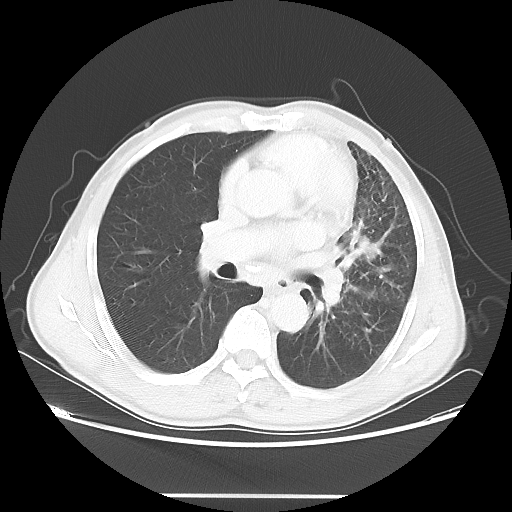
Chest CT, one axial slice. Slice 28 of 55 in the series (ordered by position). Reconstruction kernel LUNG. Lung window (W 1500 / L -600 HU). 5 mm slice thickness. 512 × 512 image matrix, field of view 398 × 398 mm. Patient: male, 60 years. Case-level facts recorded for this patient, not image findings: clinical TNM (as recorded): T3 N3 M0.
Outlined on this slice (bounding box drawn by a radiologist):
- lung tumour (recorded histology: adenocarcinoma): bounding box <346,224,382,261> (left, top, right, bottom; pixels)